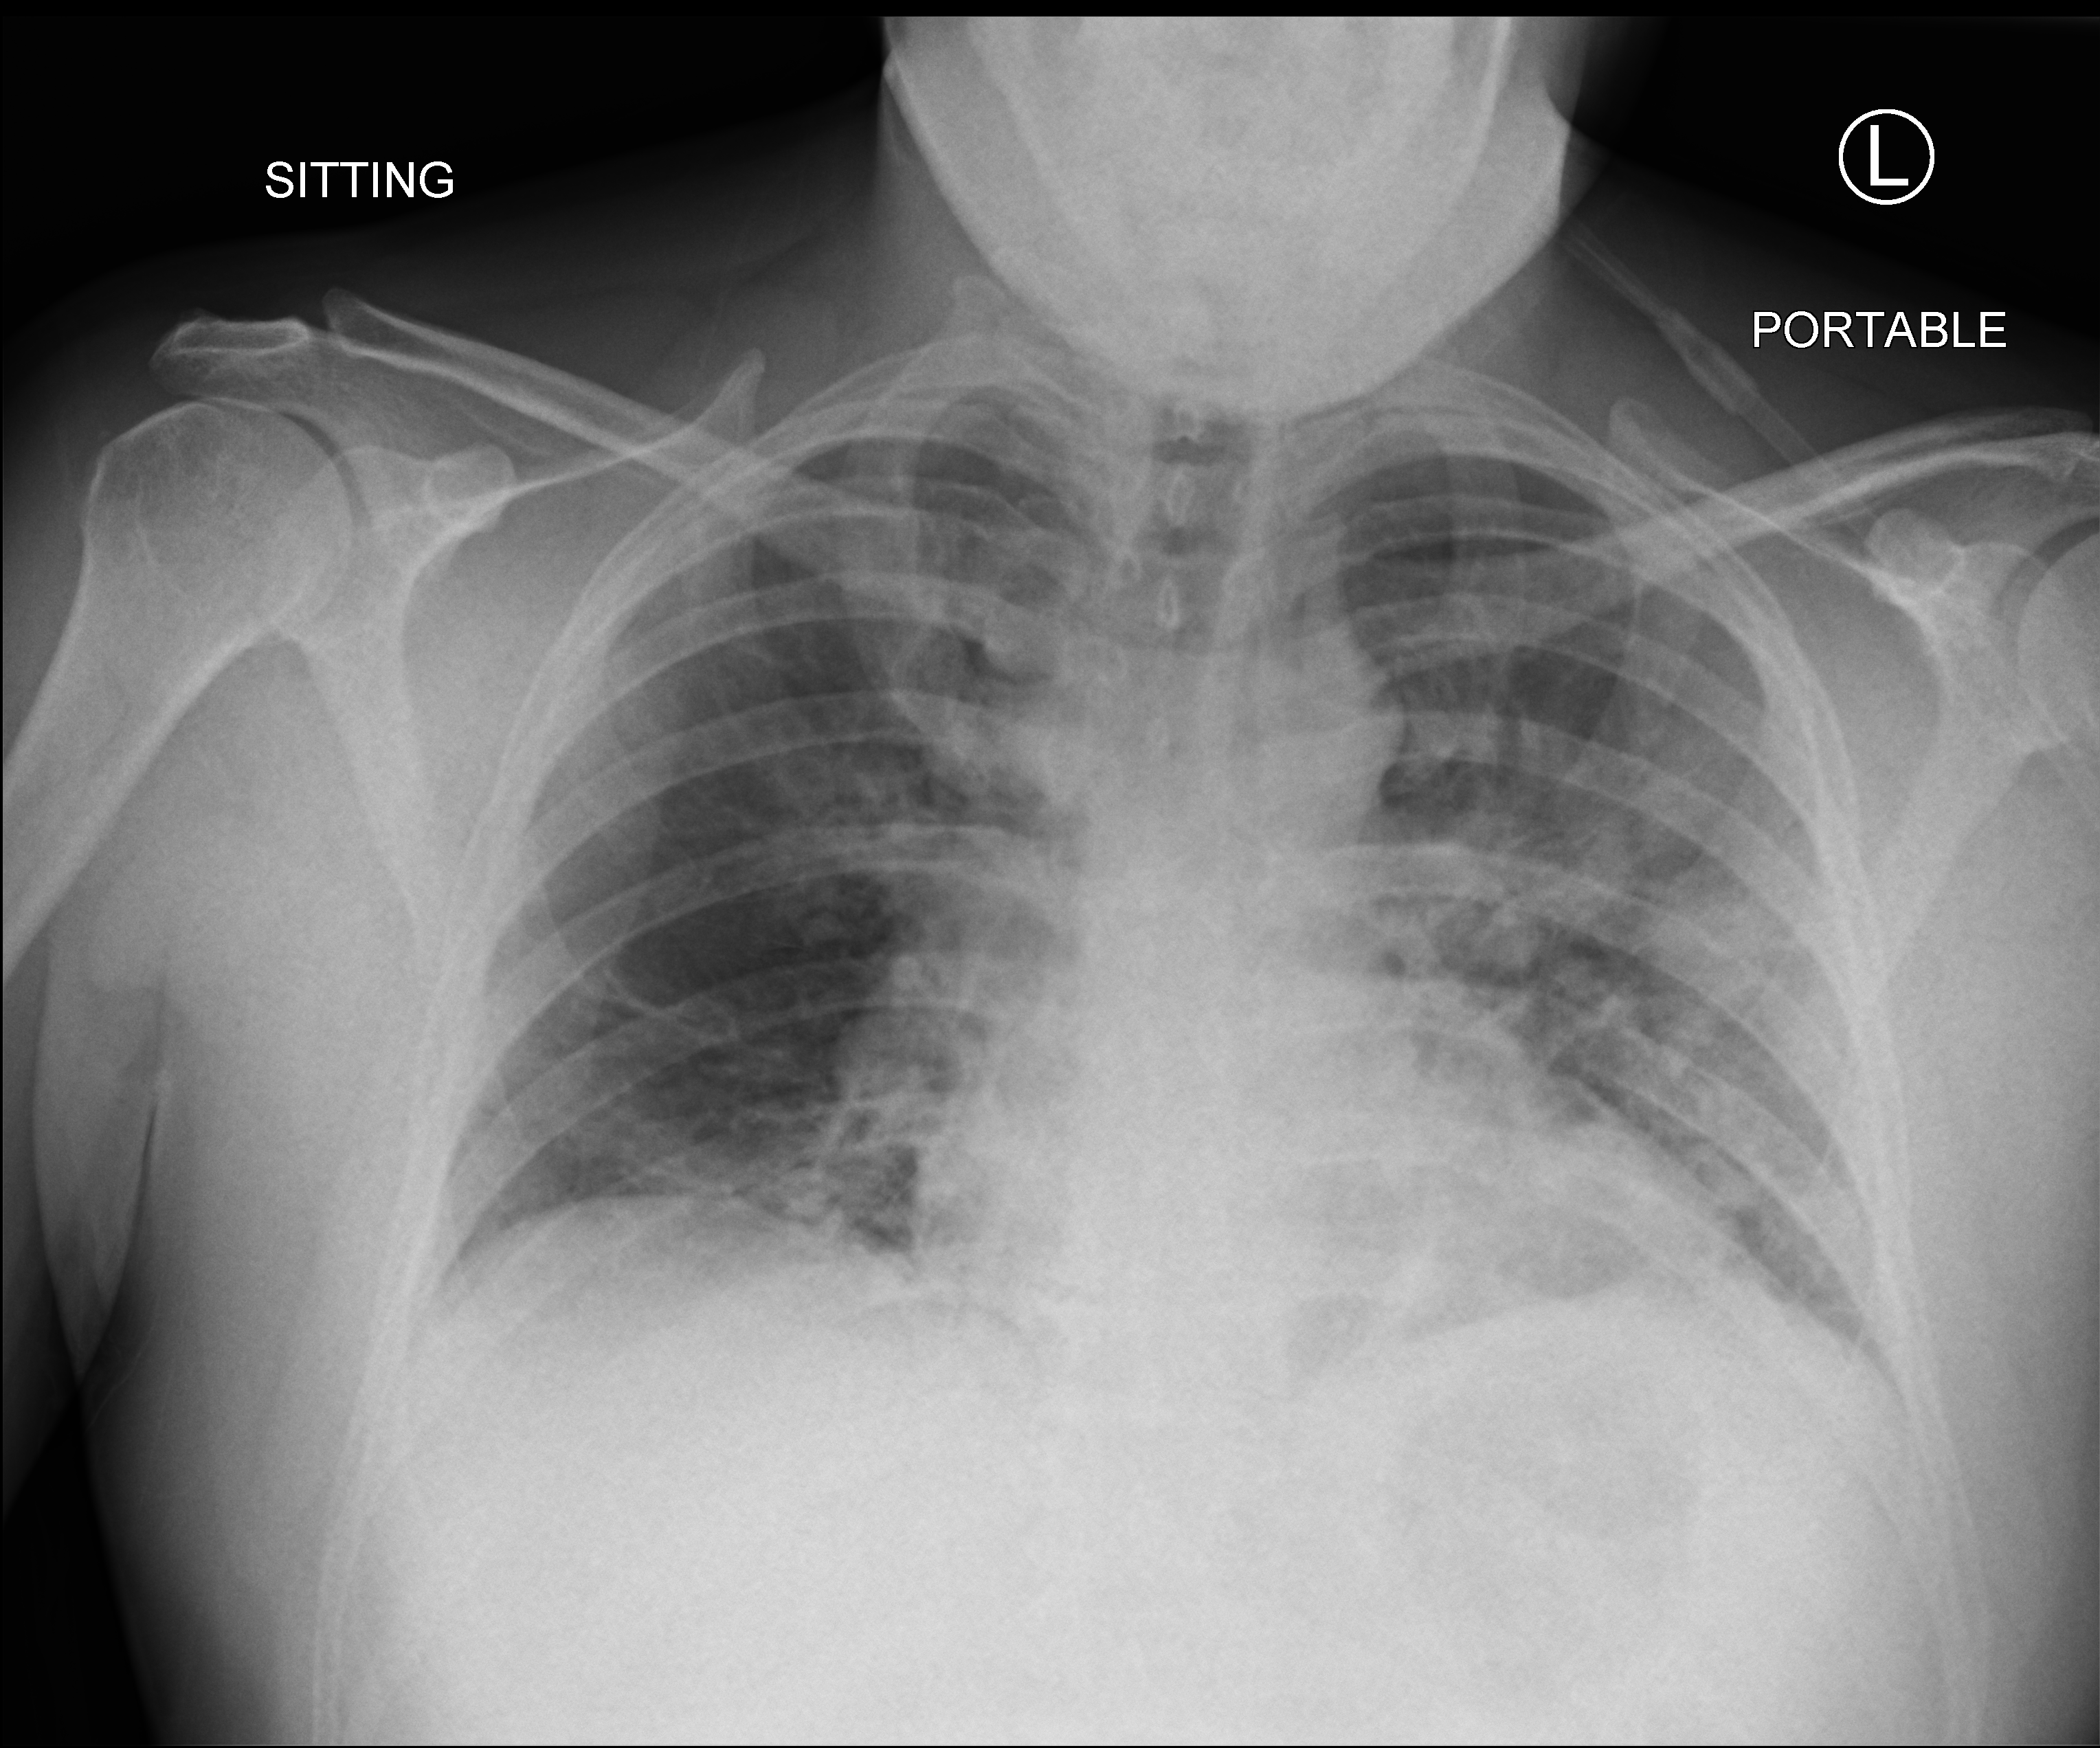
Bedside chest radiograph (computed radiography); anteroposterior (AP) projection. Male patient hospitalised with COVID-19, age 18–59 years.
Hospital-stay facts (about this admission, not read from this image; timing relative to this image not recorded):
- hypertension (admission record): no
- COPD (admission record): no
- mechanically ventilated during this hospital stay: yes